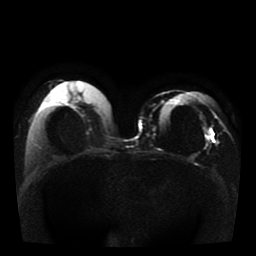
Breast MRI, one axial slice; slice 17 of 41 in the series (ordered by position); diffusion-weighted series; image 2 of 4 stored at this slice position (different b-values; order by instance number); 1.5 T; 256 × 256 image matrix. Female patient.
Structures marked on this image (outlined manually by an expert reader):
- tumour on diffusion-weighted imaging: bounding box <206,135,211,139> (left, top, right, bottom; pixels)